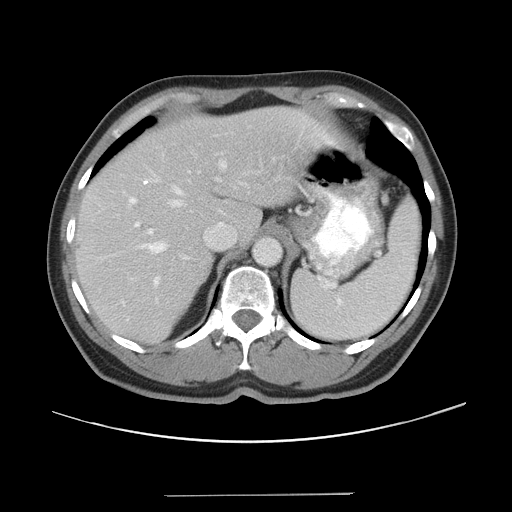
Contrast-enhanced abdominal CT, one axial slice; slice 30 of 43 in the series (ordered by position); reconstruction kernel STANDARD; soft-tissue window (W 400 / L 40 HU); 5 mm slice thickness; 512 × 512 image matrix, field of view 409 × 409 mm. Male patient, age 65 years. Case-level facts recorded for this patient, not image findings: diagnosis: colorectal cancer liver metastases, imaged before liver resection.
Outlined on this slice (outlined manually by an expert reader):
- hepatic veins: bounding box (x1, y1, x2, y2) in pixels: (139, 164, 226, 254)
- liver: (75, 109, 320, 342)
- planned liver remnant (the part of the liver to remain after resection): (75, 109, 320, 341)
- portal vein (with intrahepatic branches): (129, 149, 280, 300)